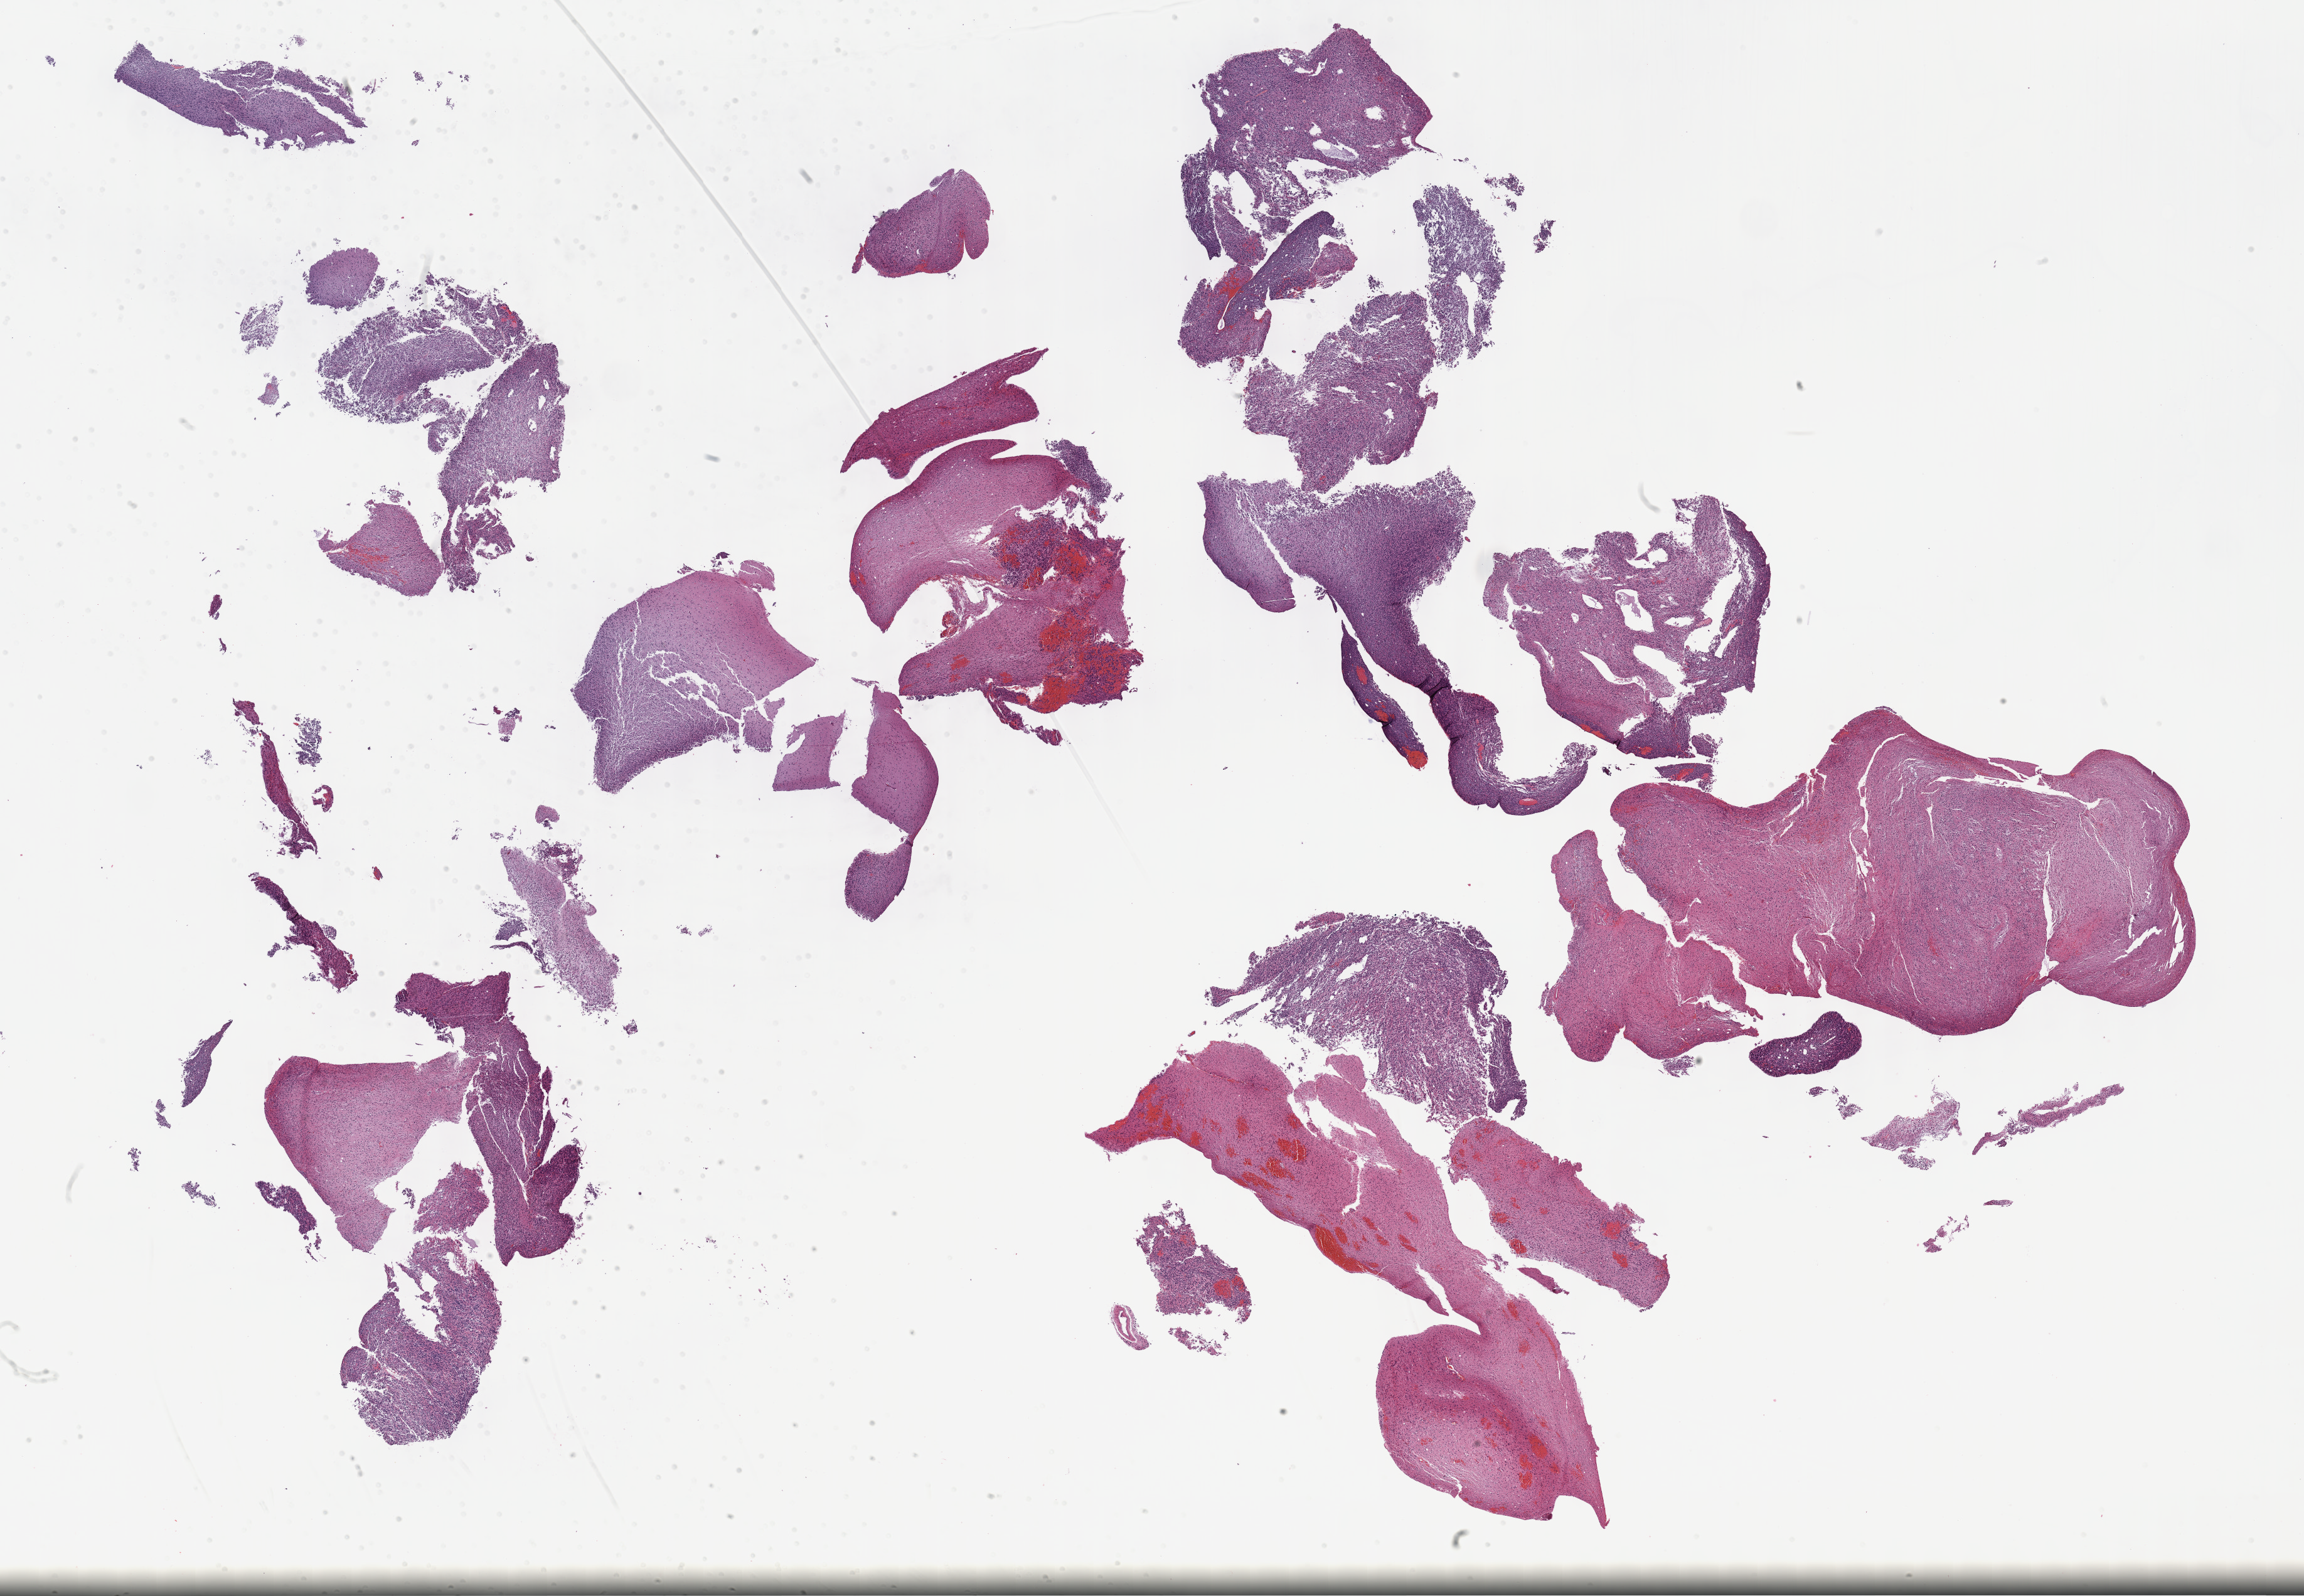
Hematoxylin and eosin (H&E) stained whole-slide image — low-resolution overview of the scanned area, about 29.7 x 20.6 mm, formalin-fixed paraffin-embedded (FFPE) diagnostic section, brain, primary tumour sample. Female, age 44 years at initial diagnosis. Histologic grade: G3 (poorly differentiated).
Laterality: left. Diagnosis: Astrocytoma, anaplastic (cerebrum).